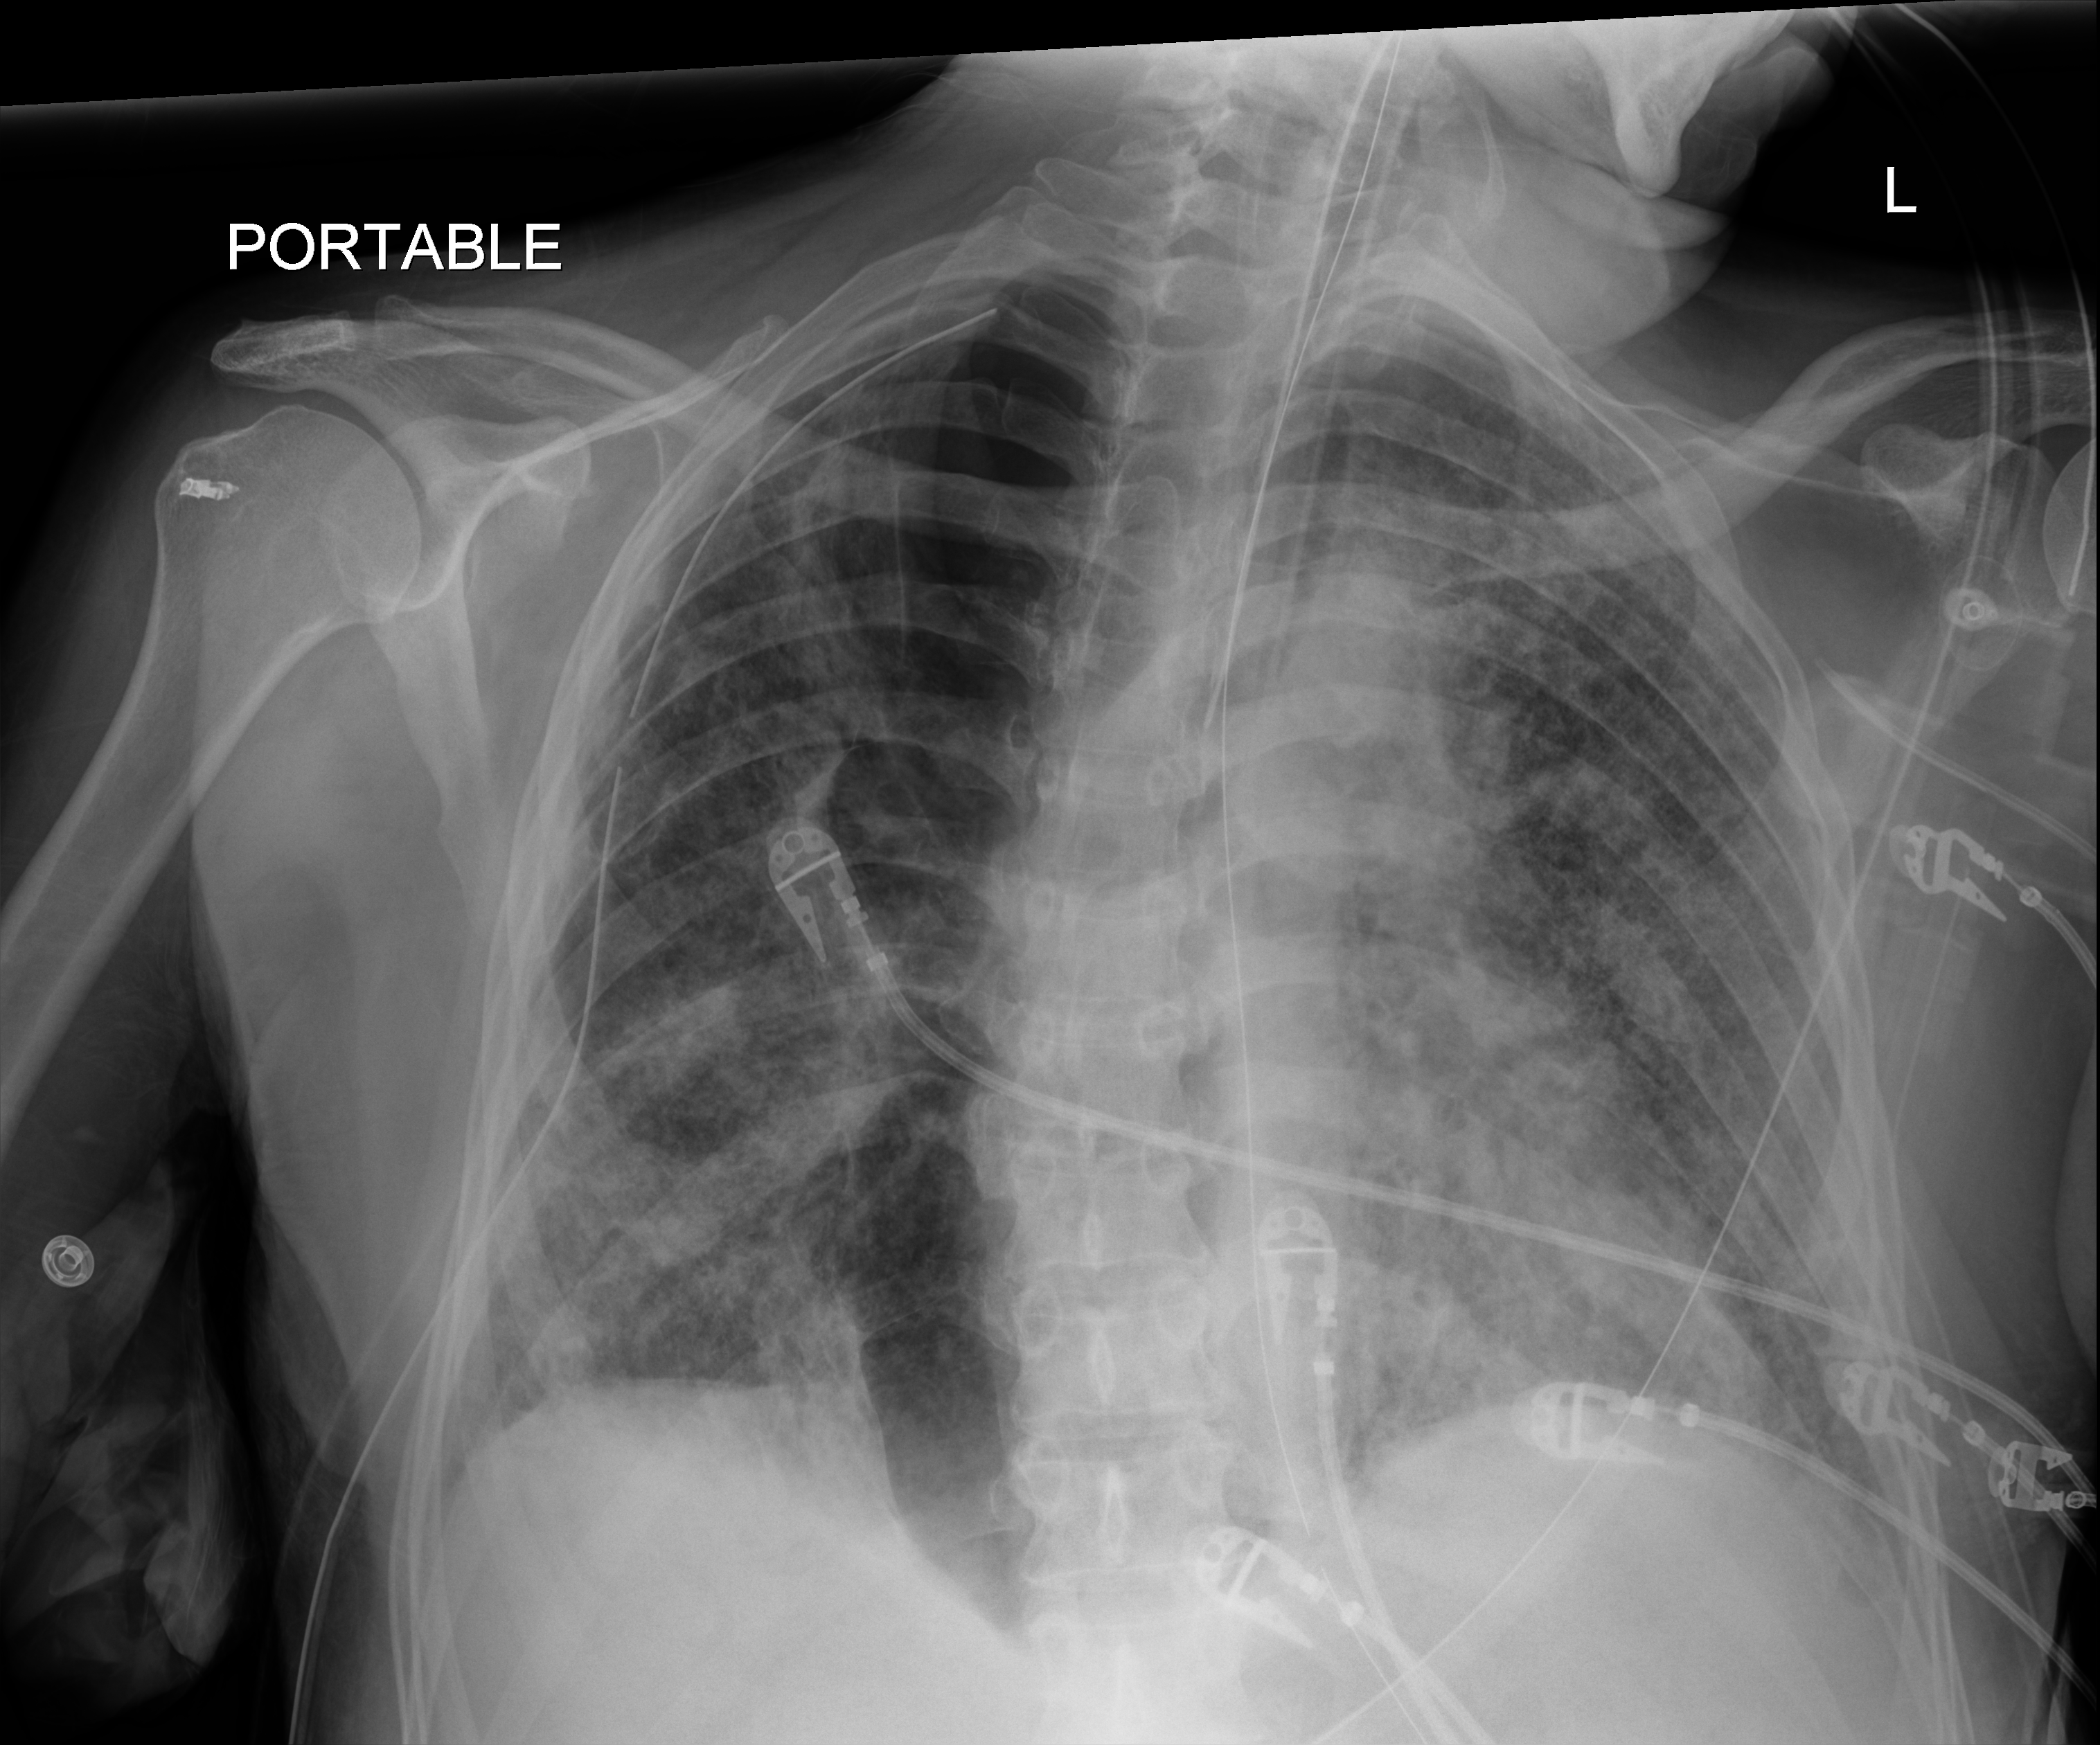
Chest X-ray (portable). Patient hospitalised with COVID-19; male, aged 60–74 years.
Admission-level facts for this patient (not findings on this image; timing relative to this image not recorded):
- length of hospital stay: 65 days
- other chronic lung disease (admission record): yes
- mechanically ventilated during this hospital stay: yes